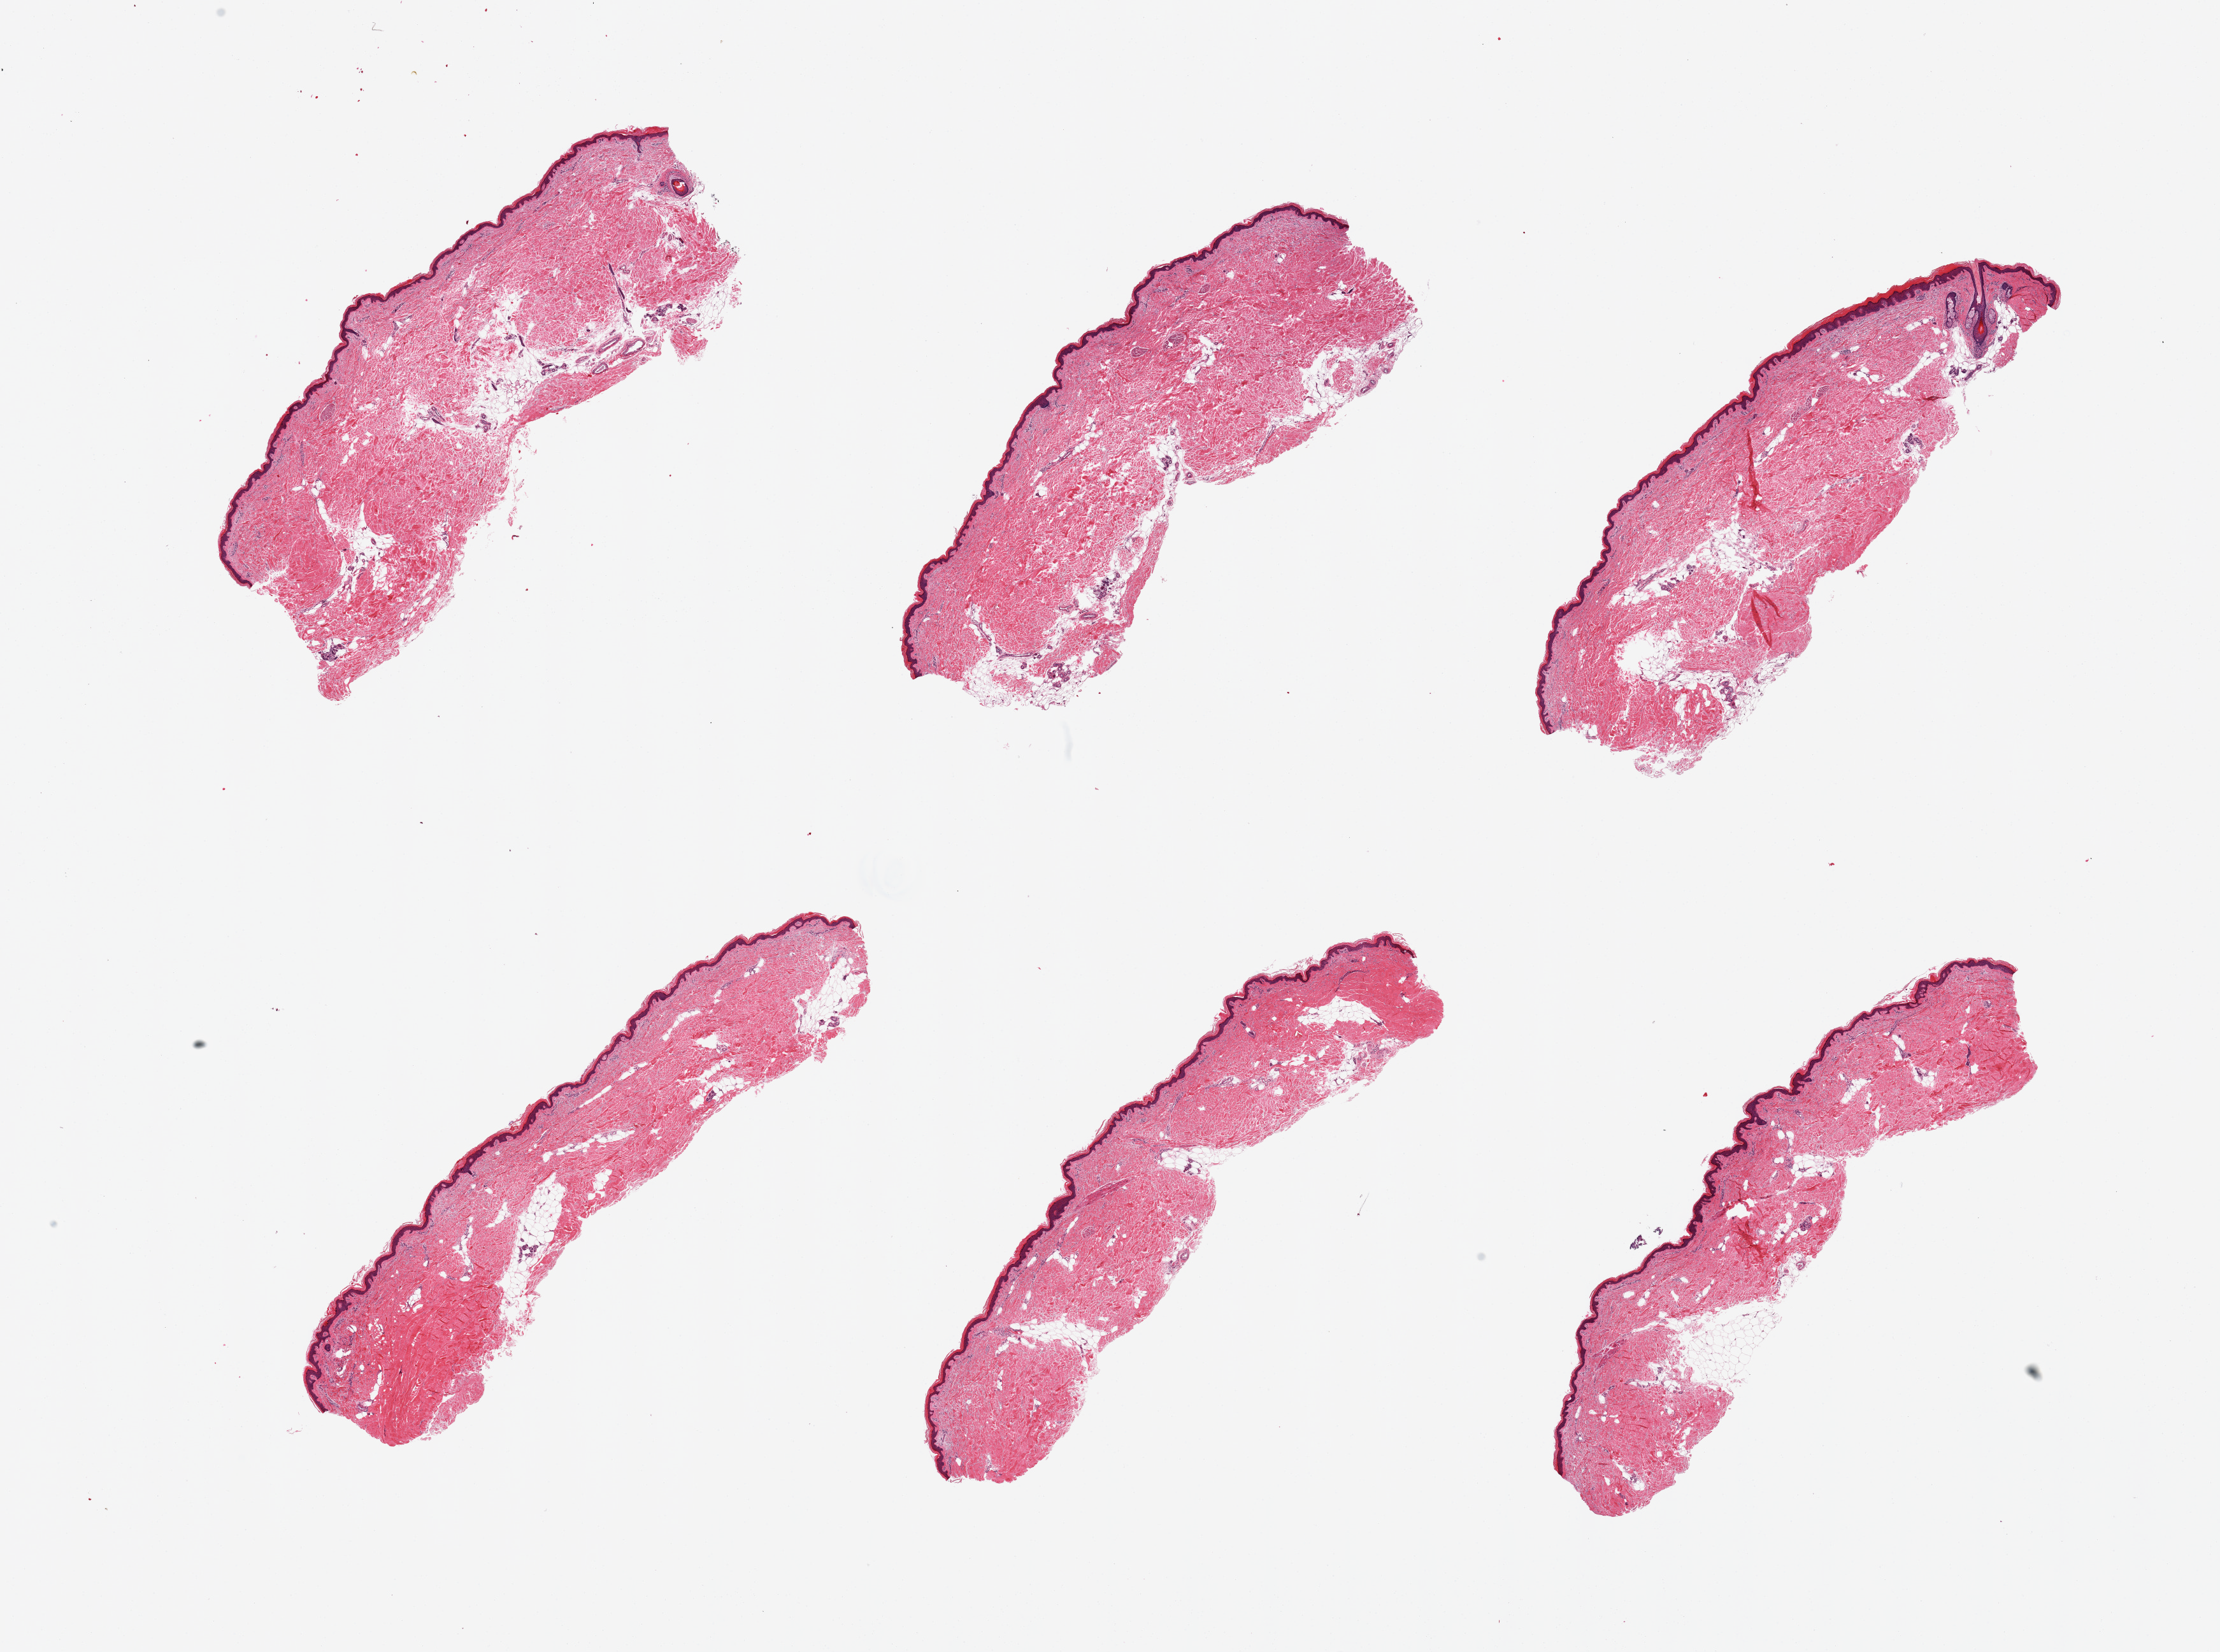
Hematoxylin and eosin (H&E) whole-slide image, a low-resolution overview of the entire scanned area, about 27.6 x 20.5 mm (from a 20x scan); PAXgene-fixed, paraffin-embedded tissue; target tissue: skin of lower leg; tissue donor sample. Donor sex: female.
Review note (as recorded): 6 pieces; well dissected; 10% intradermal fat.